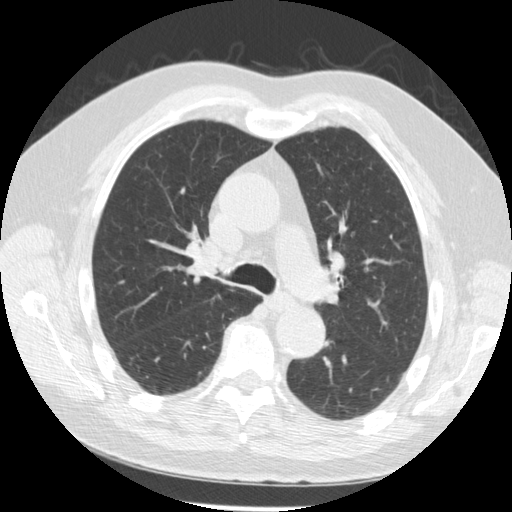
Low-dose screening chest CT, one axial slice; position 172 of 259 along the scan axis; reconstruction kernel STANDARD; 120 kVp; lung window (W 1500 / L -600 HU); 2.5 mm slice thickness; 512 × 512 image matrix.
Annotated regions visible in this slice (outlined manually by an expert reader):
- lesion 2 (tumor, hilum of right lung): bounding box <189,248,220,275> (left, top, right, bottom; pixels)